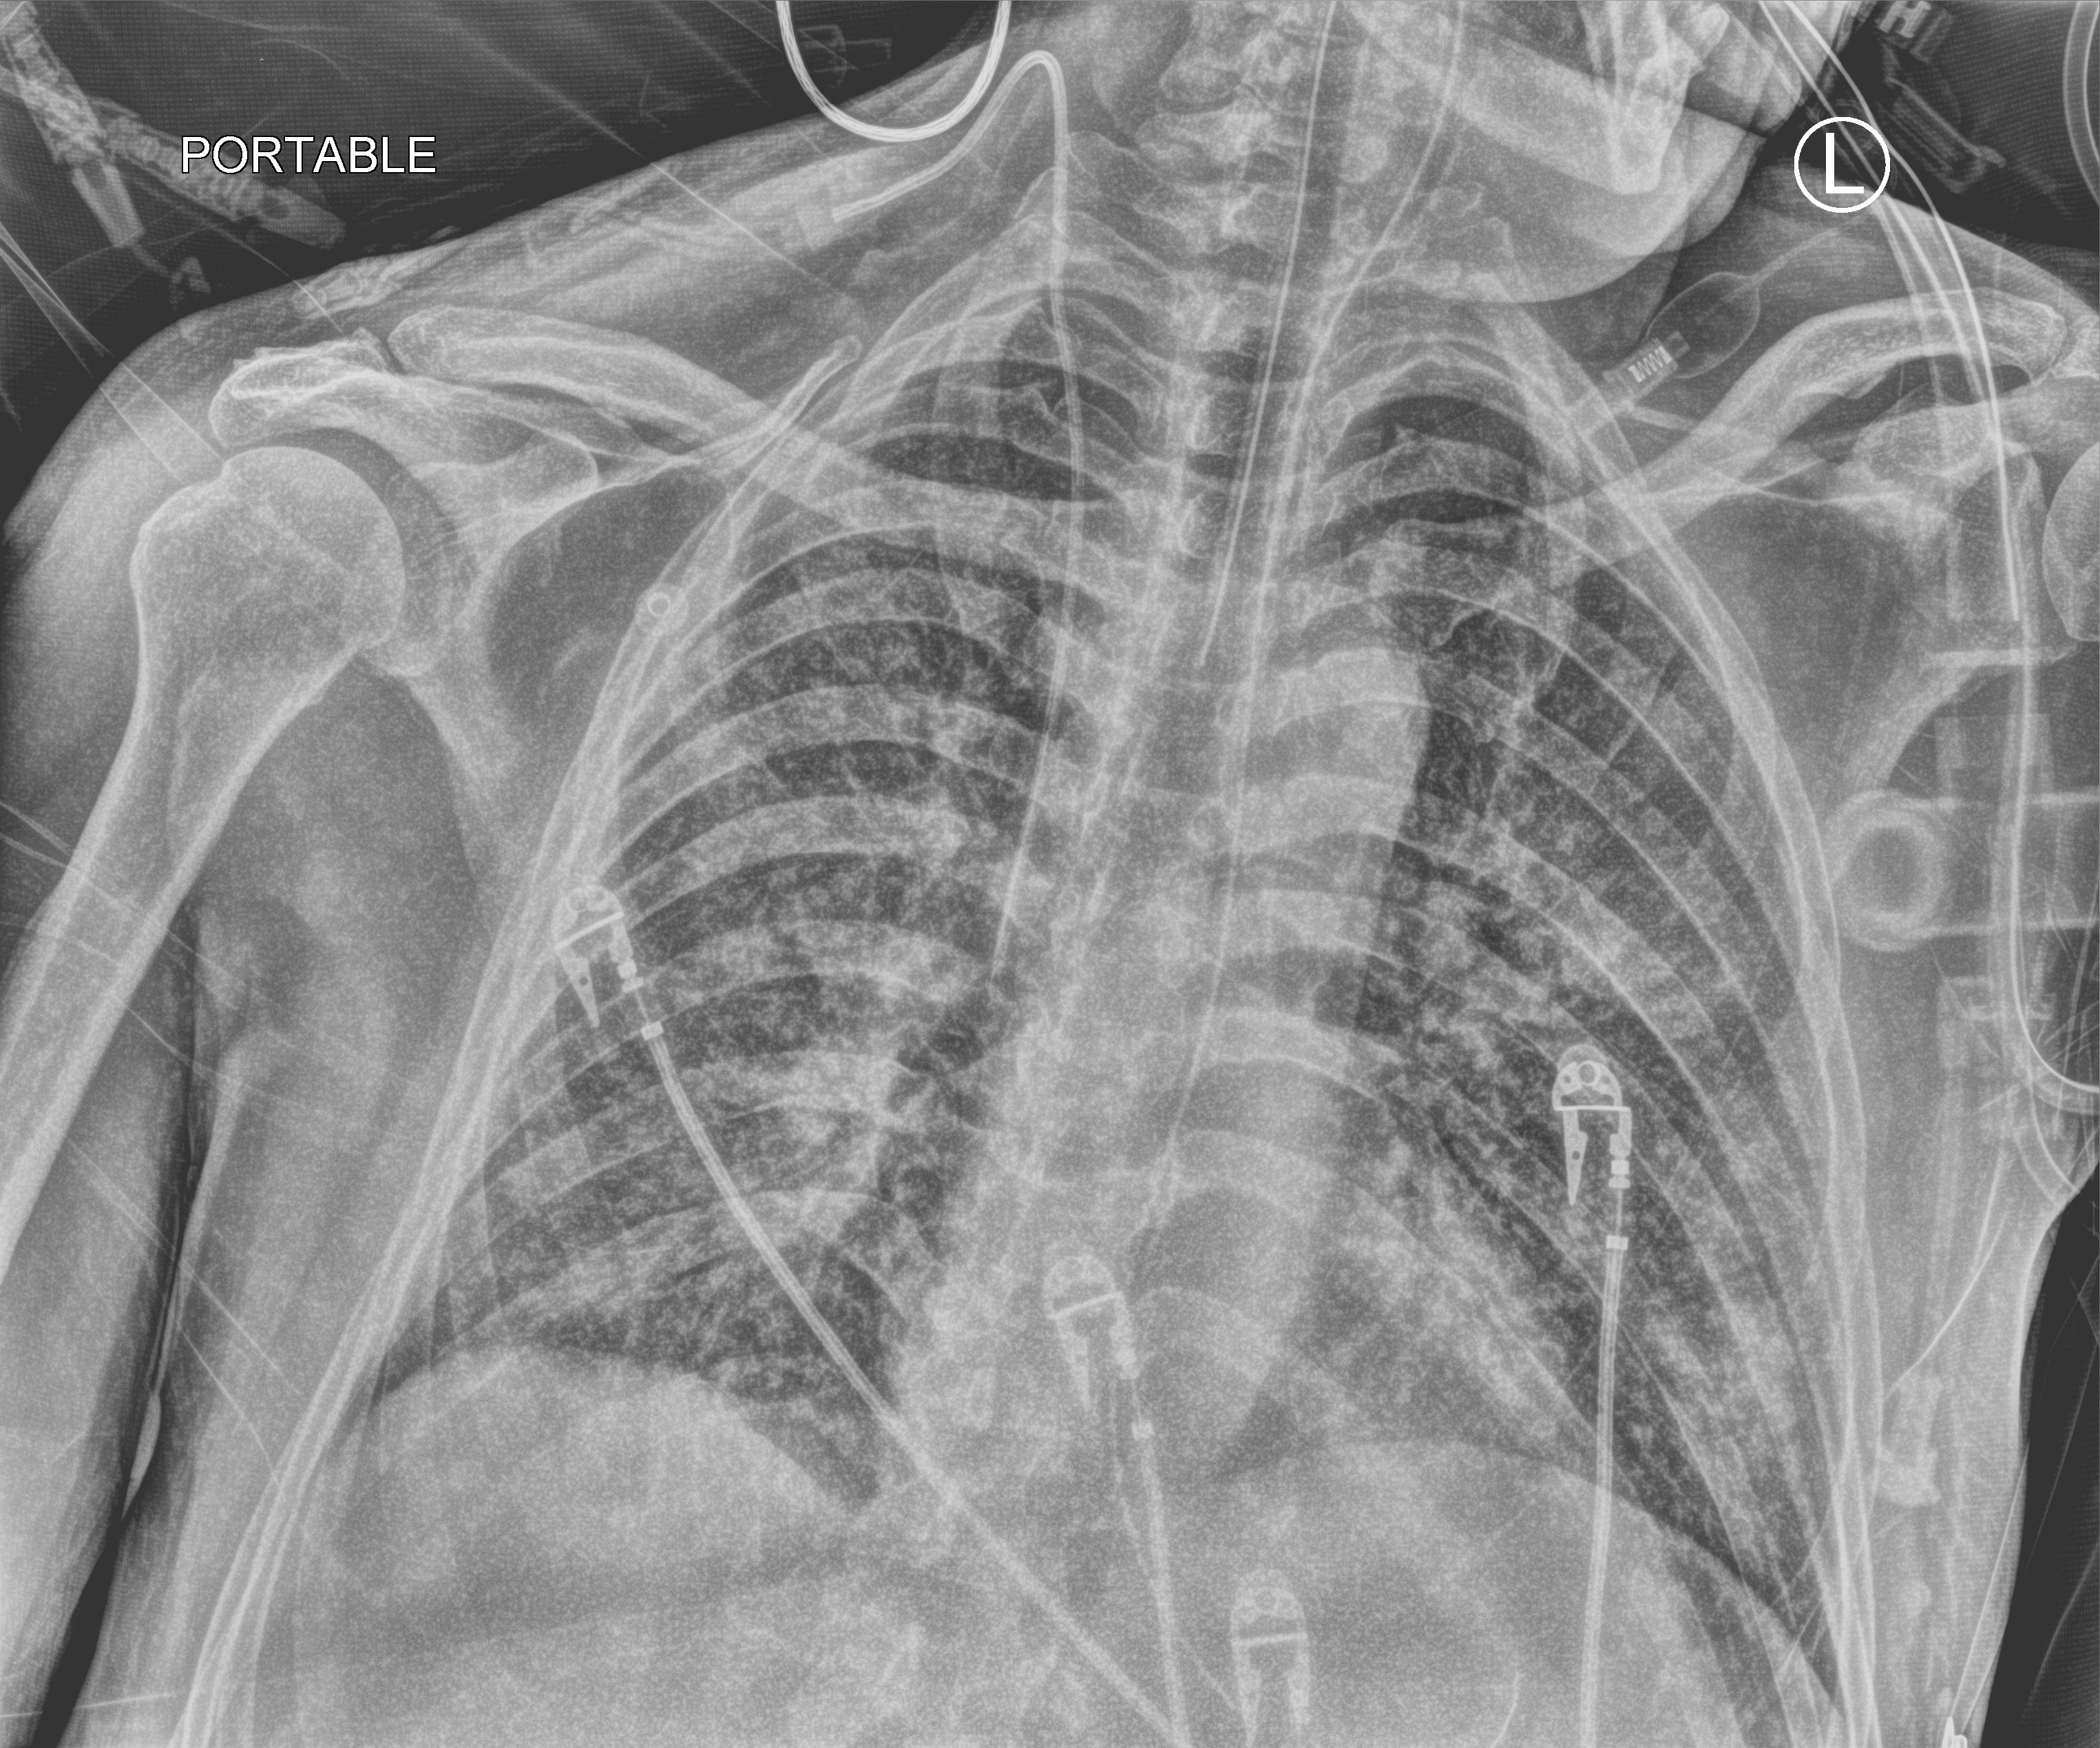
Portable chest radiograph. Patient hospitalised with COVID-19; male, aged 60–74 years.
Hospital-stay facts (about this admission, not read from this image; timing relative to this image not recorded): admitted to intensive care during this hospital stay: yes; mechanically ventilated during this hospital stay: yes.